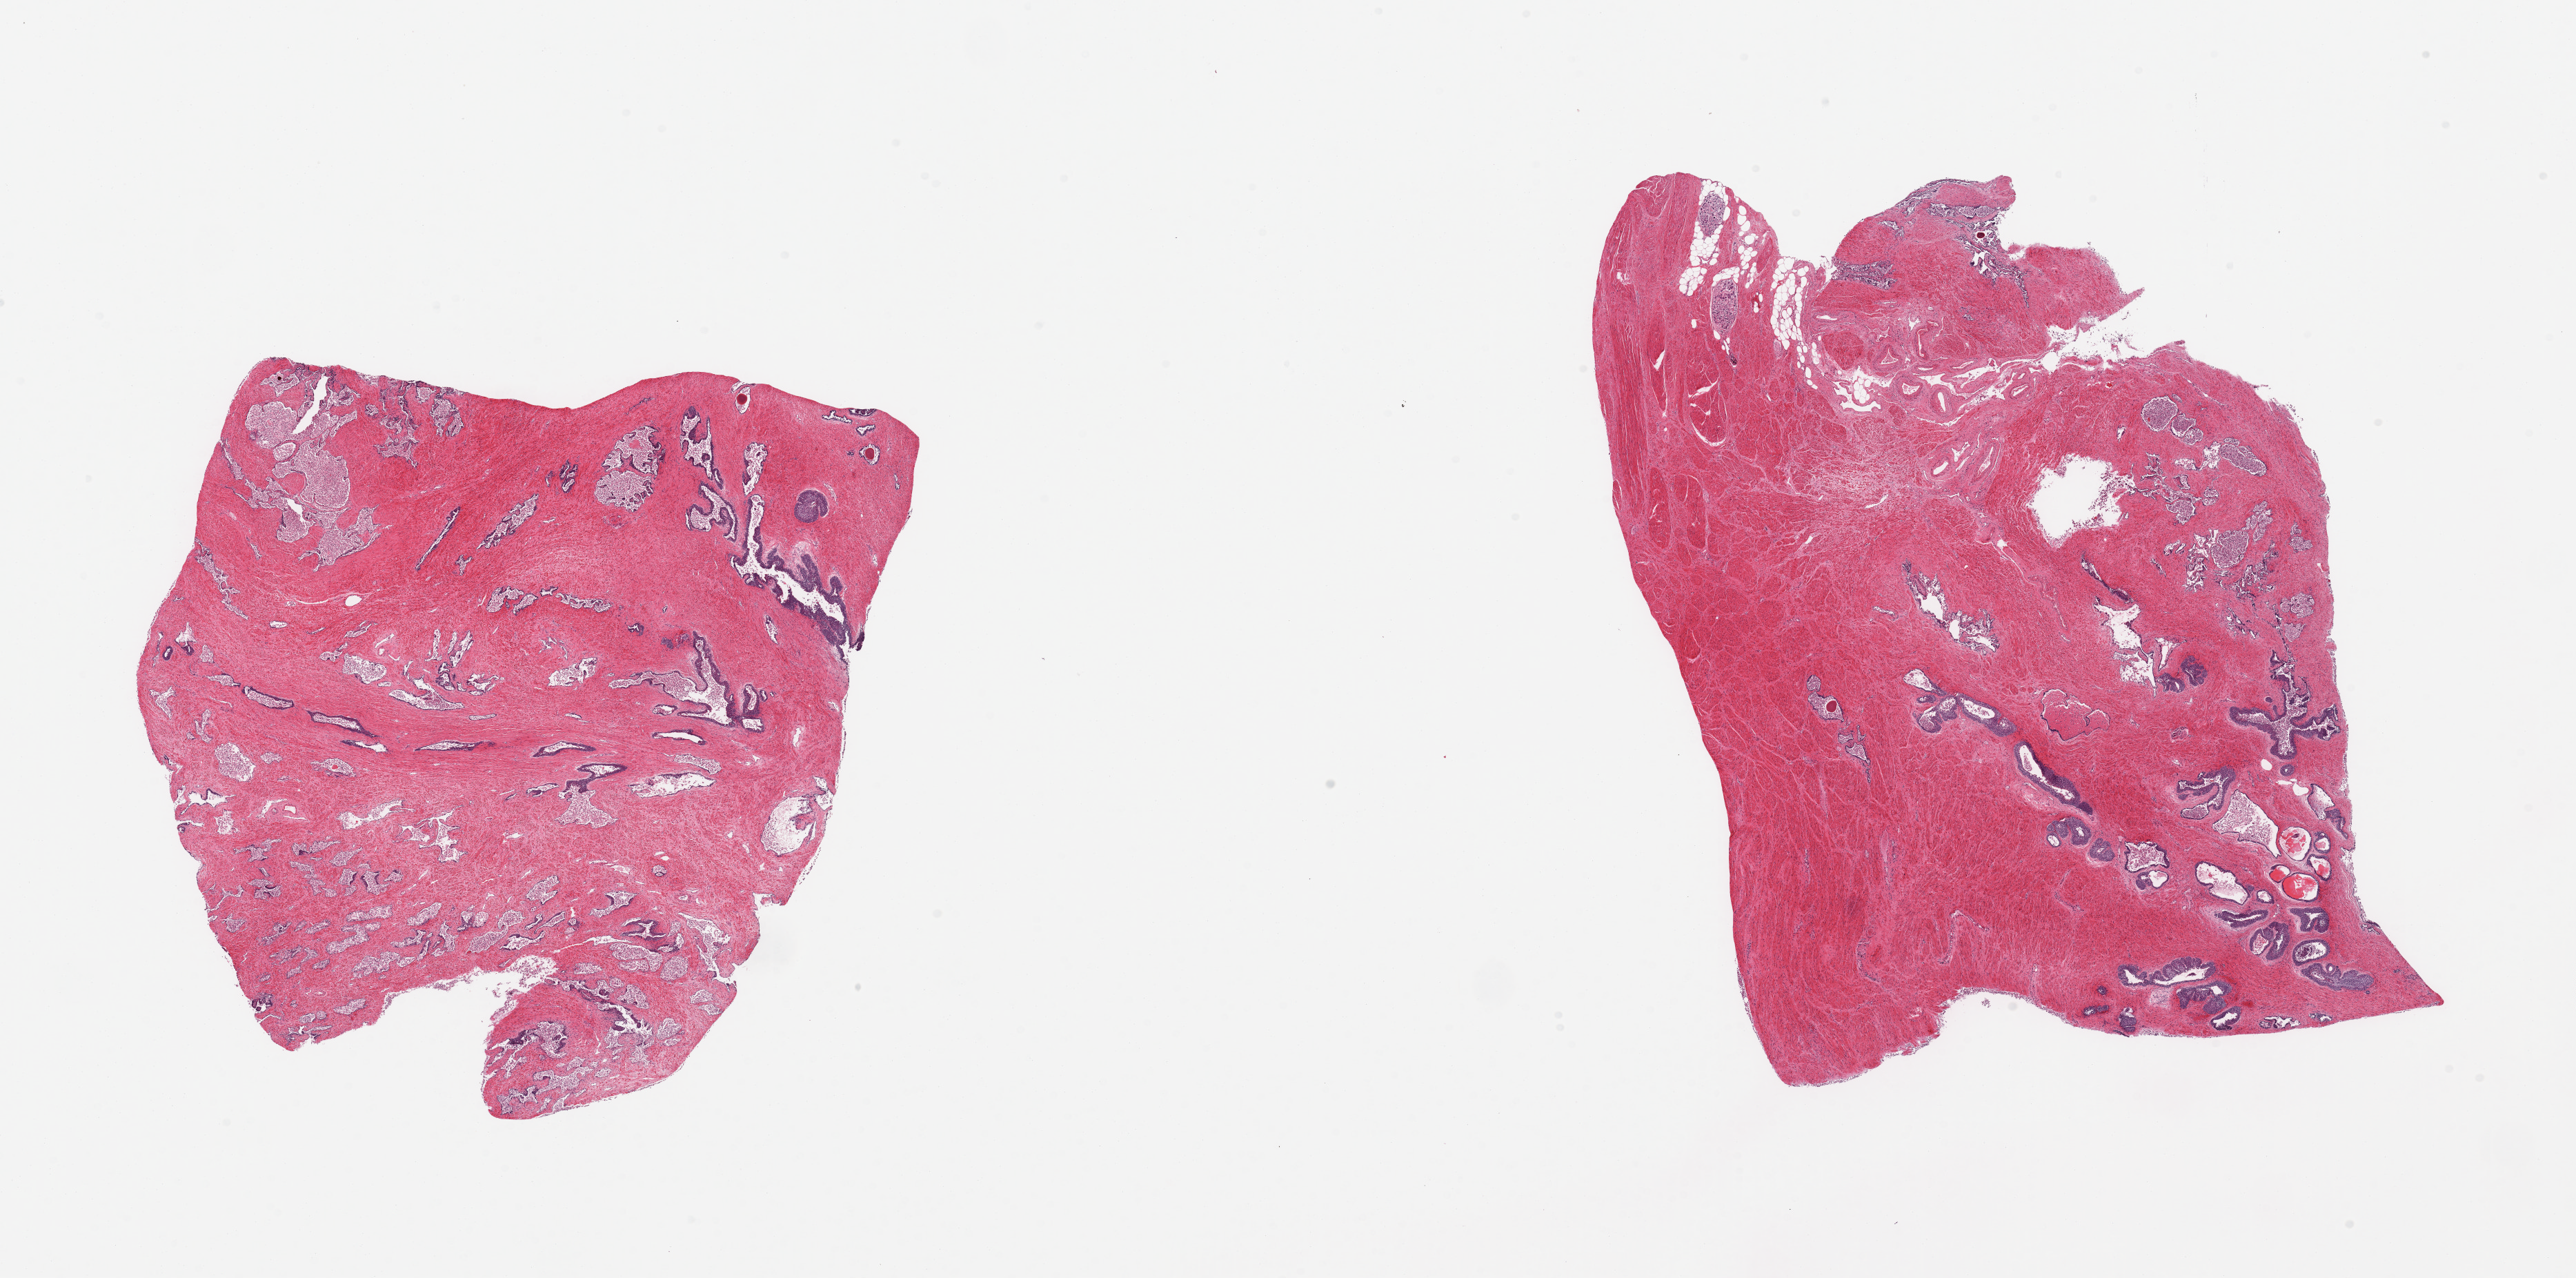
Haematoxylin and eosin whole-slide image, brightfield, shown as a low-resolution overview of the whole scanned area (about 29.5 x 14.6 mm); PAXgene-fixed paraffin-embedded (PFPE) section; section of prostate (target tissue); donor tissue sample. Male donor.
- pathologist's review note for this sample: 2 pieces; fibromuscular stroma and autolyzed glandular component ~75%, ~25% well preserved glandular component lined by urothelial epithelium, ganglion